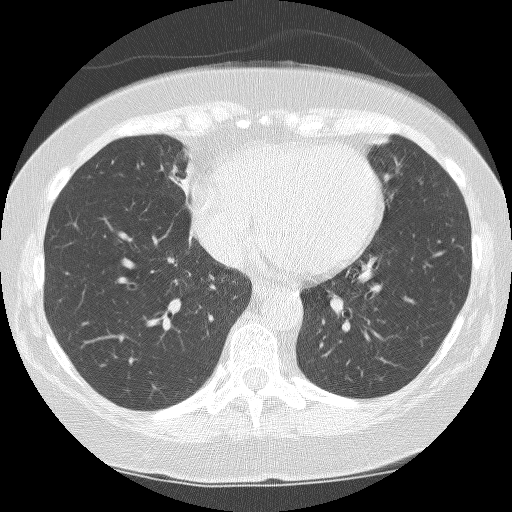
Low-dose screening chest CT, one axial slice; reconstruction kernel BONE; lung window (W 1500 / L -600 HU); 512 × 512 image matrix, field of view 299 × 299 mm.
Annotated regions visible in this slice (expert manual segmentation):
- lesion 1 (tumor, hilum of right lung): bounding box <167,161,194,202> (left, top, right, bottom; pixels)